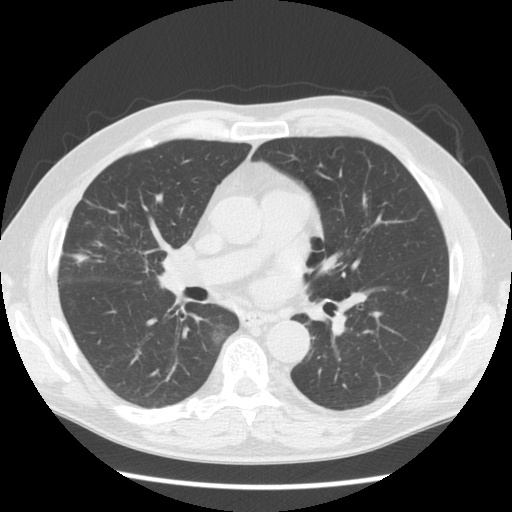
Low-dose screening chest CT, one axial slice. Slice 82 of 146 in the series (ordered by position). 120 kVp. Lung window (W 1500 / L -600 HU). 512 × 512 image matrix, field of view 350 × 350 mm.
Outlined on this slice (expert manual segmentation):
- lesion 1 (tumor, middle lobe of right lung): bounding box (x1, y1, x2, y2) in pixels: (74, 255, 87, 263)